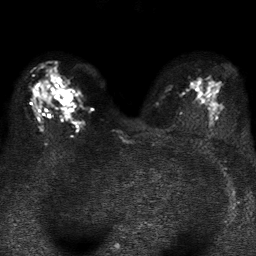
Breast MRI, one axial slice. Position 23 of 37 along the scan axis. Diffusion-weighted series; image 2 of 4 stored at this slice position (different b-values; order by instance number). 1.5 T. 256 × 256 image matrix. Female patient.
Outlined on this slice (manually delineated by an expert):
- tumour on diffusion-weighted imaging: bounding box [x1, y1, x2, y2] px = [55, 89, 71, 98]